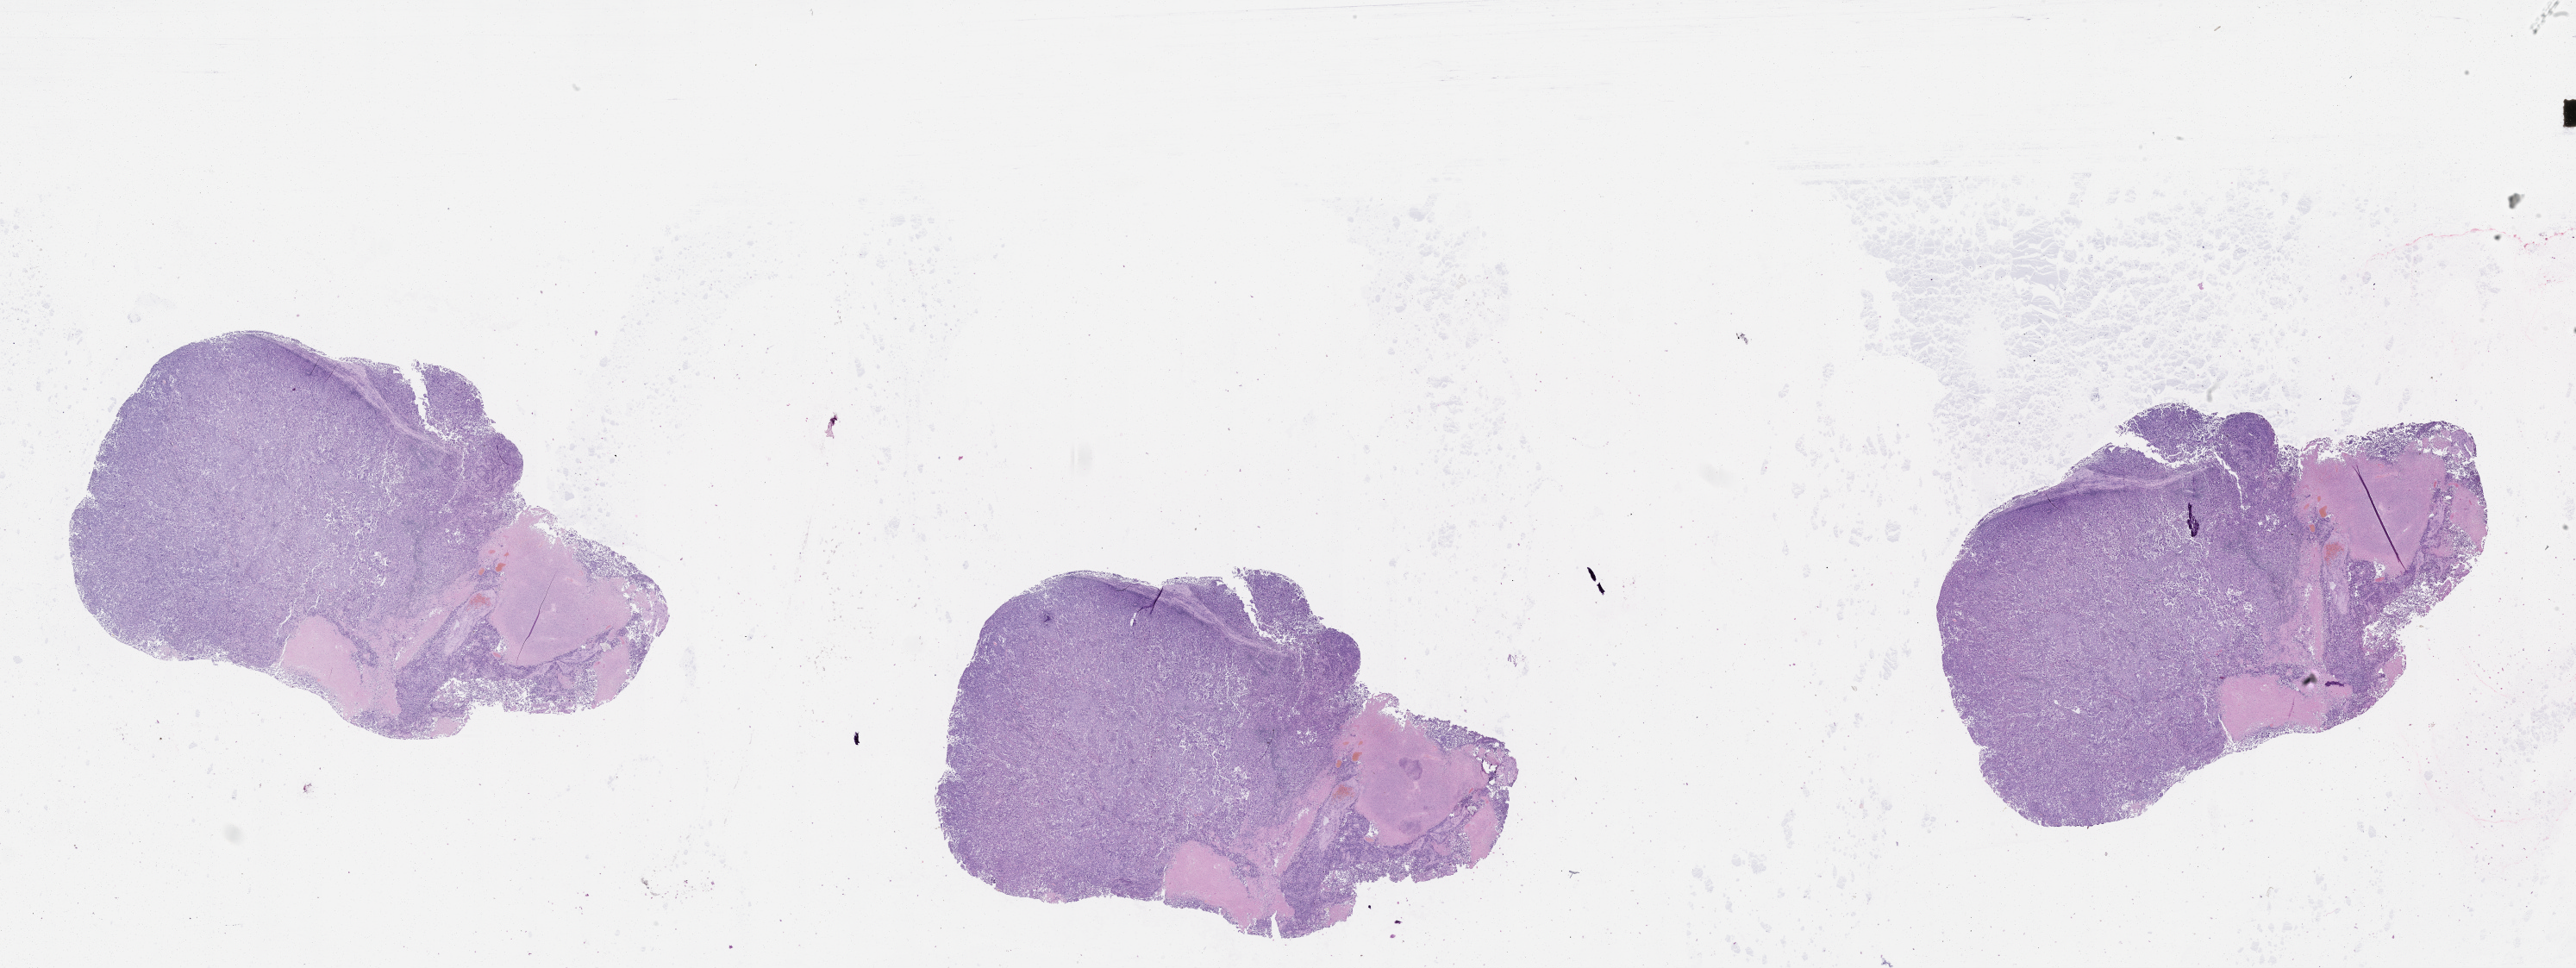
Digitized Hematoxylin and eosin (H&E) stained tissue section (whole slide), a low-resolution overview of the entire scanned area, about 48.1 x 18.1 mm. Patient: female, age 62 years.
Patient diagnosis: Malignant melanoma, NOS.